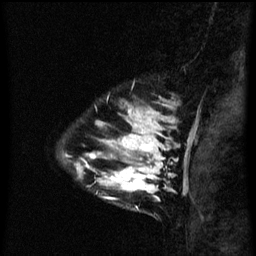
Breast MRI (dynamic contrast-enhanced), one sagittal slice. Position 14 of 60 along the scan axis. Dynamic contrast-enhanced series, image 2 of 3 at this slice position (ordered by acquisition). 1.5 T. TE 4.2 ms, TR 8 ms. 2.3 mm slice thickness. 256 × 256 image matrix, field of view 180 × 180 mm. Female patient, age 33 years.
Annotated regions visible in this slice (semi-automatically segmented with operator editing):
- analysis volume of interest (the breast-tissue region the enhancement analysis was run in; not a lesion): bounding box [x1, y1, x2, y2] px = [71, 118, 171, 211]
- tumour enhancement mask (voxels above the 70 % enhancement threshold inside the analysis volume of interest): [77, 118, 171, 199]